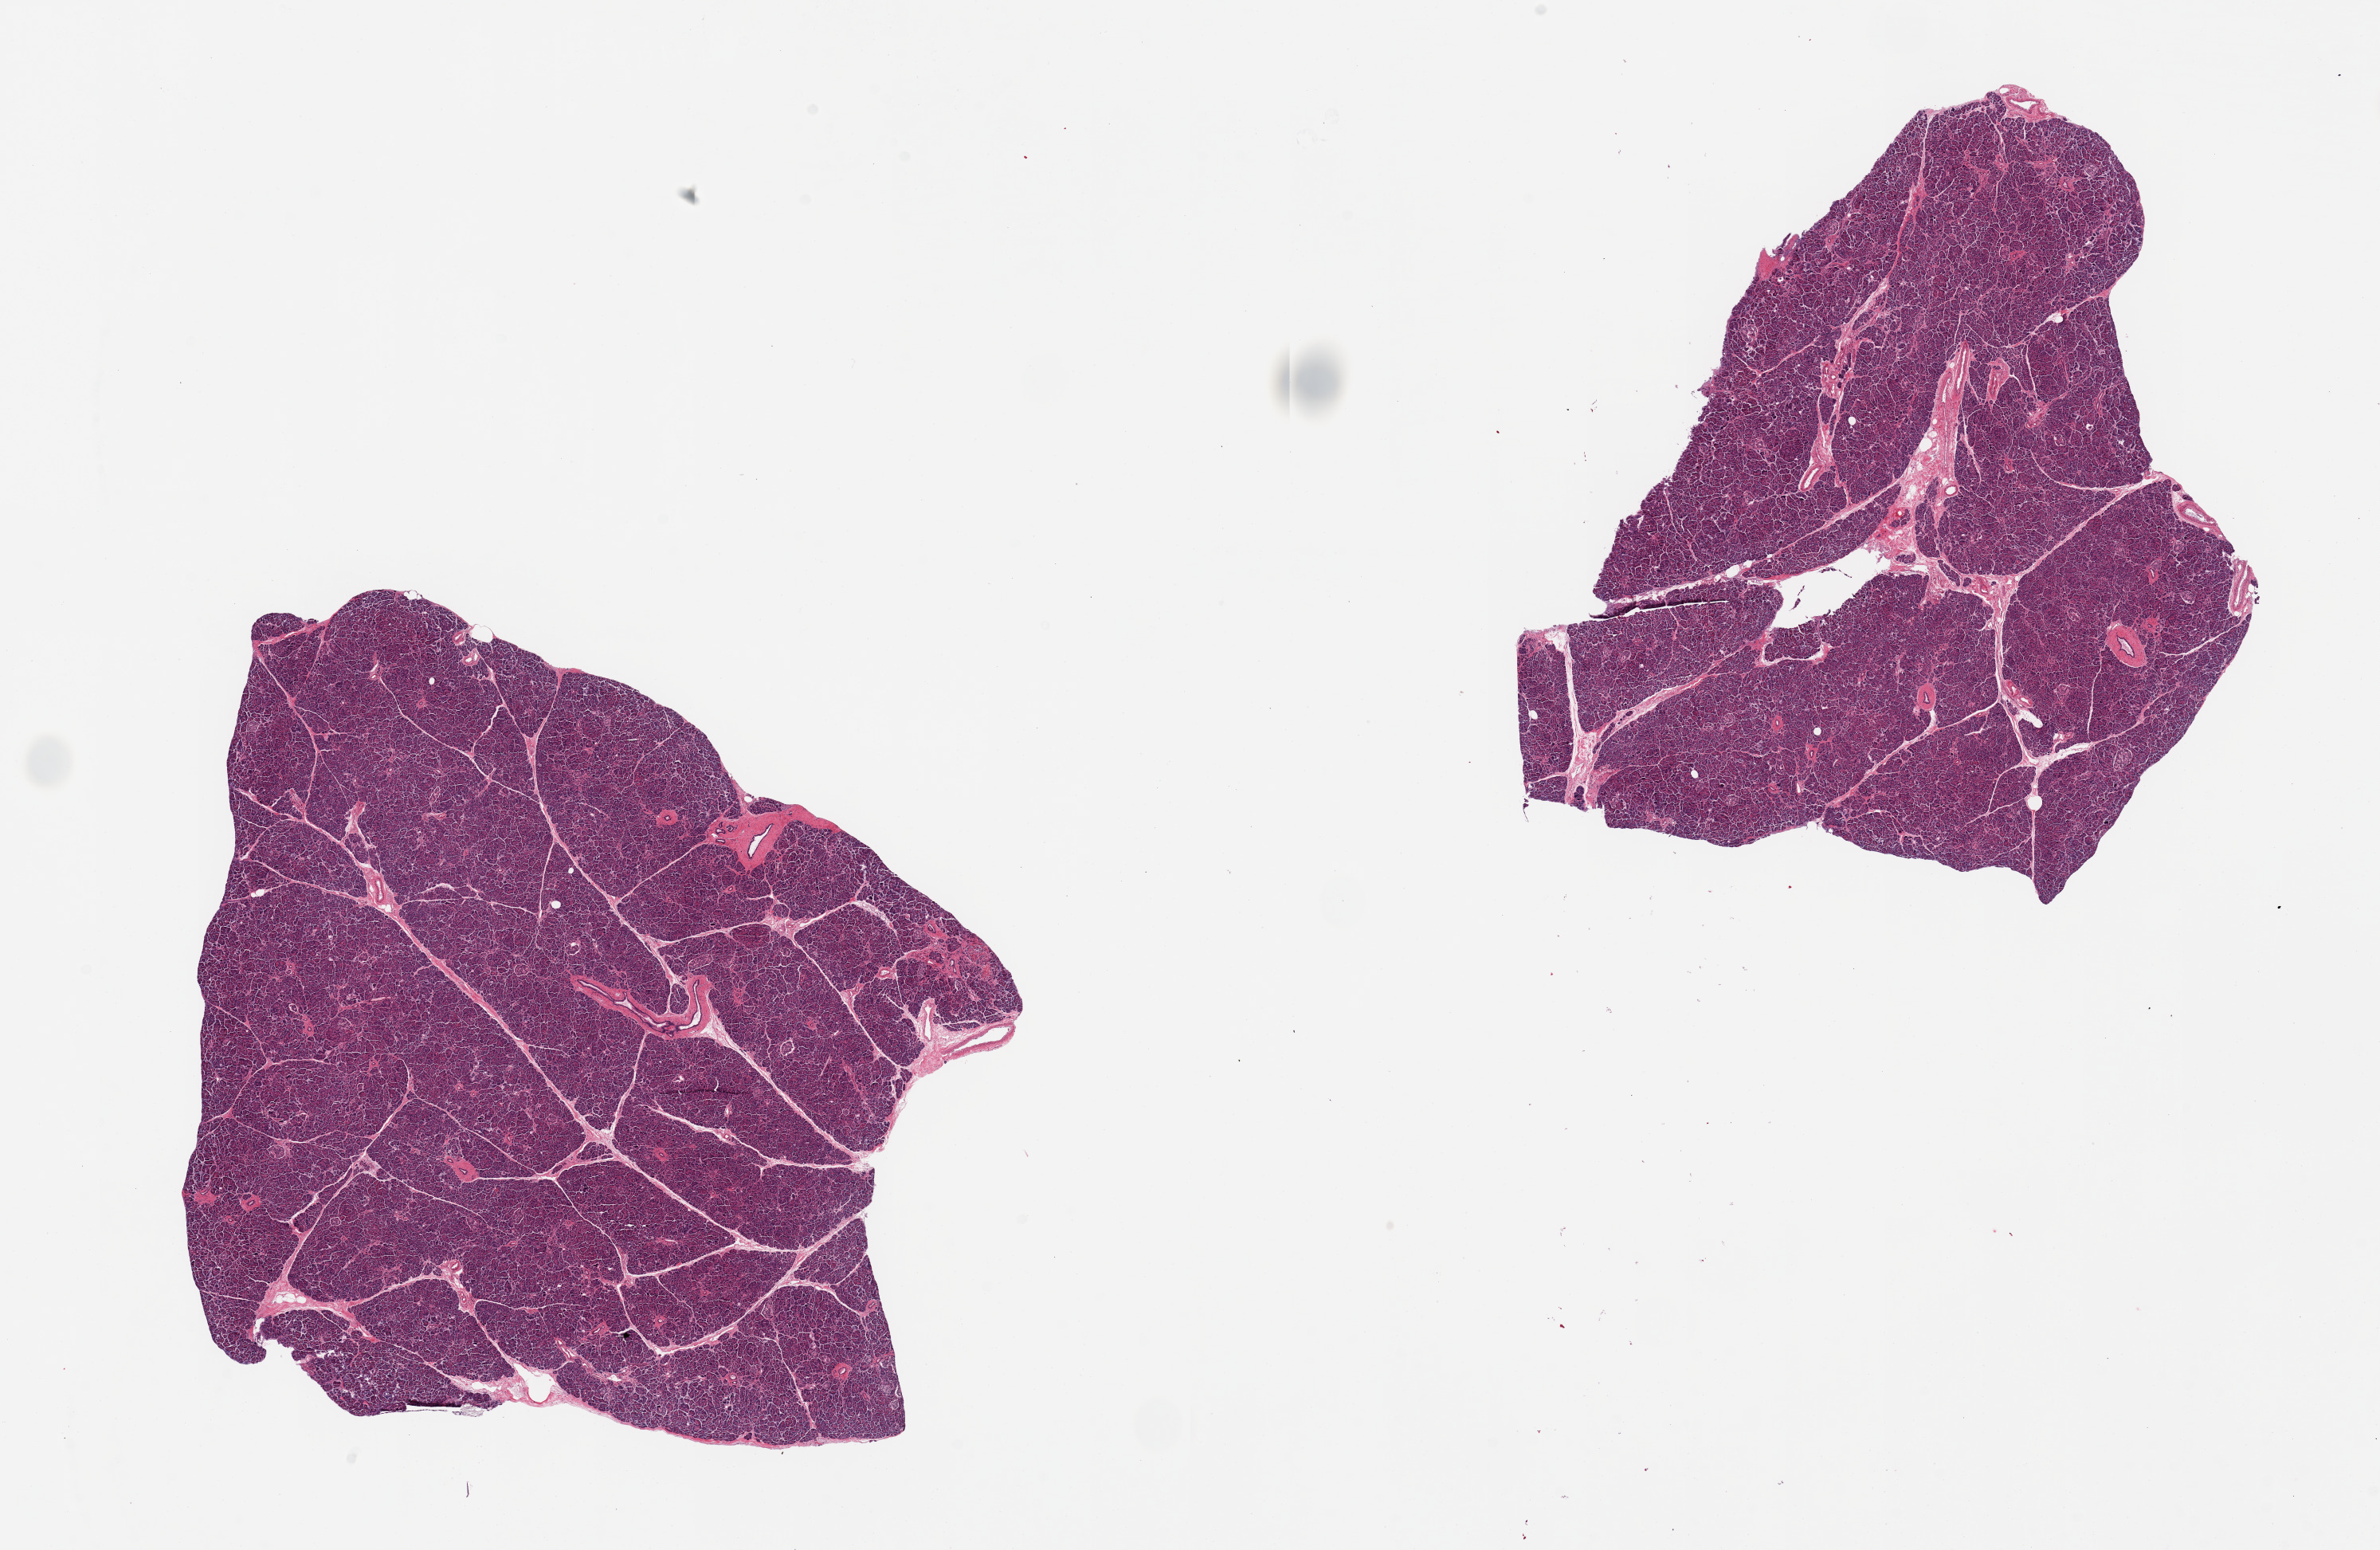
Digitized hematoxylin and eosin (H&E)-stained section, brightfield, whole scanned area (about 23.6 x 15.4 mm) shown as a low-resolution overview. PAXgene-fixed paraffin-embedded (PFPE) section. Sampled site (target tissue): pancreas. Donor tissue sample. Female donor.
Reviewer comment on this tissue sample: 2 pieces, 9x8.5 & 9x6mm; well trimmed, no adipose.